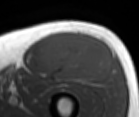
MRI of an extremity soft-tissue mass, one axial slice; position 51 of 86 along the scan axis; MR volume resampled by the dataset authors to the PET/CT grid (not the native acquisition matrix); 3.27 mm slice thickness; 139 × 117 image matrix, field of view 136 × 114 mm. Male patient. Case-level facts recorded for this patient, not image findings: histological type: extraskeletal osteosarcoma; grade: high; site of the primary tumour: thigh.
Annotated regions visible in this slice (expert contour drawn on MRI and transferred to this co-registered scan by the dataset authors):
- gross tumour volume (mass): bounding box [x1, y1, x2, y2] px = [40, 32, 112, 83]